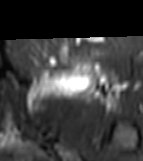
MRI of an extremity soft-tissue mass, one axial slice; position 45 of 81 along the scan axis; STIR; MR volume resampled by the dataset authors to the PET/CT grid (not the native acquisition matrix); 3.27 mm slice thickness; 143 × 161 image matrix, field of view 140 × 157 mm. Female patient. Case-level facts recorded for this patient, not image findings: histological type: myxofibrosarcoma; grade: intermediate; site of the primary tumour: left thigh.
Annotated regions visible in this slice (expert contour drawn on MRI and transferred to this co-registered scan by the dataset authors):
- gross tumour volume including surrounding oedema: box from (x=24, y=62) to (x=125, y=109) px
- gross tumour volume (mass): (x=54, y=62)–(x=86, y=91)